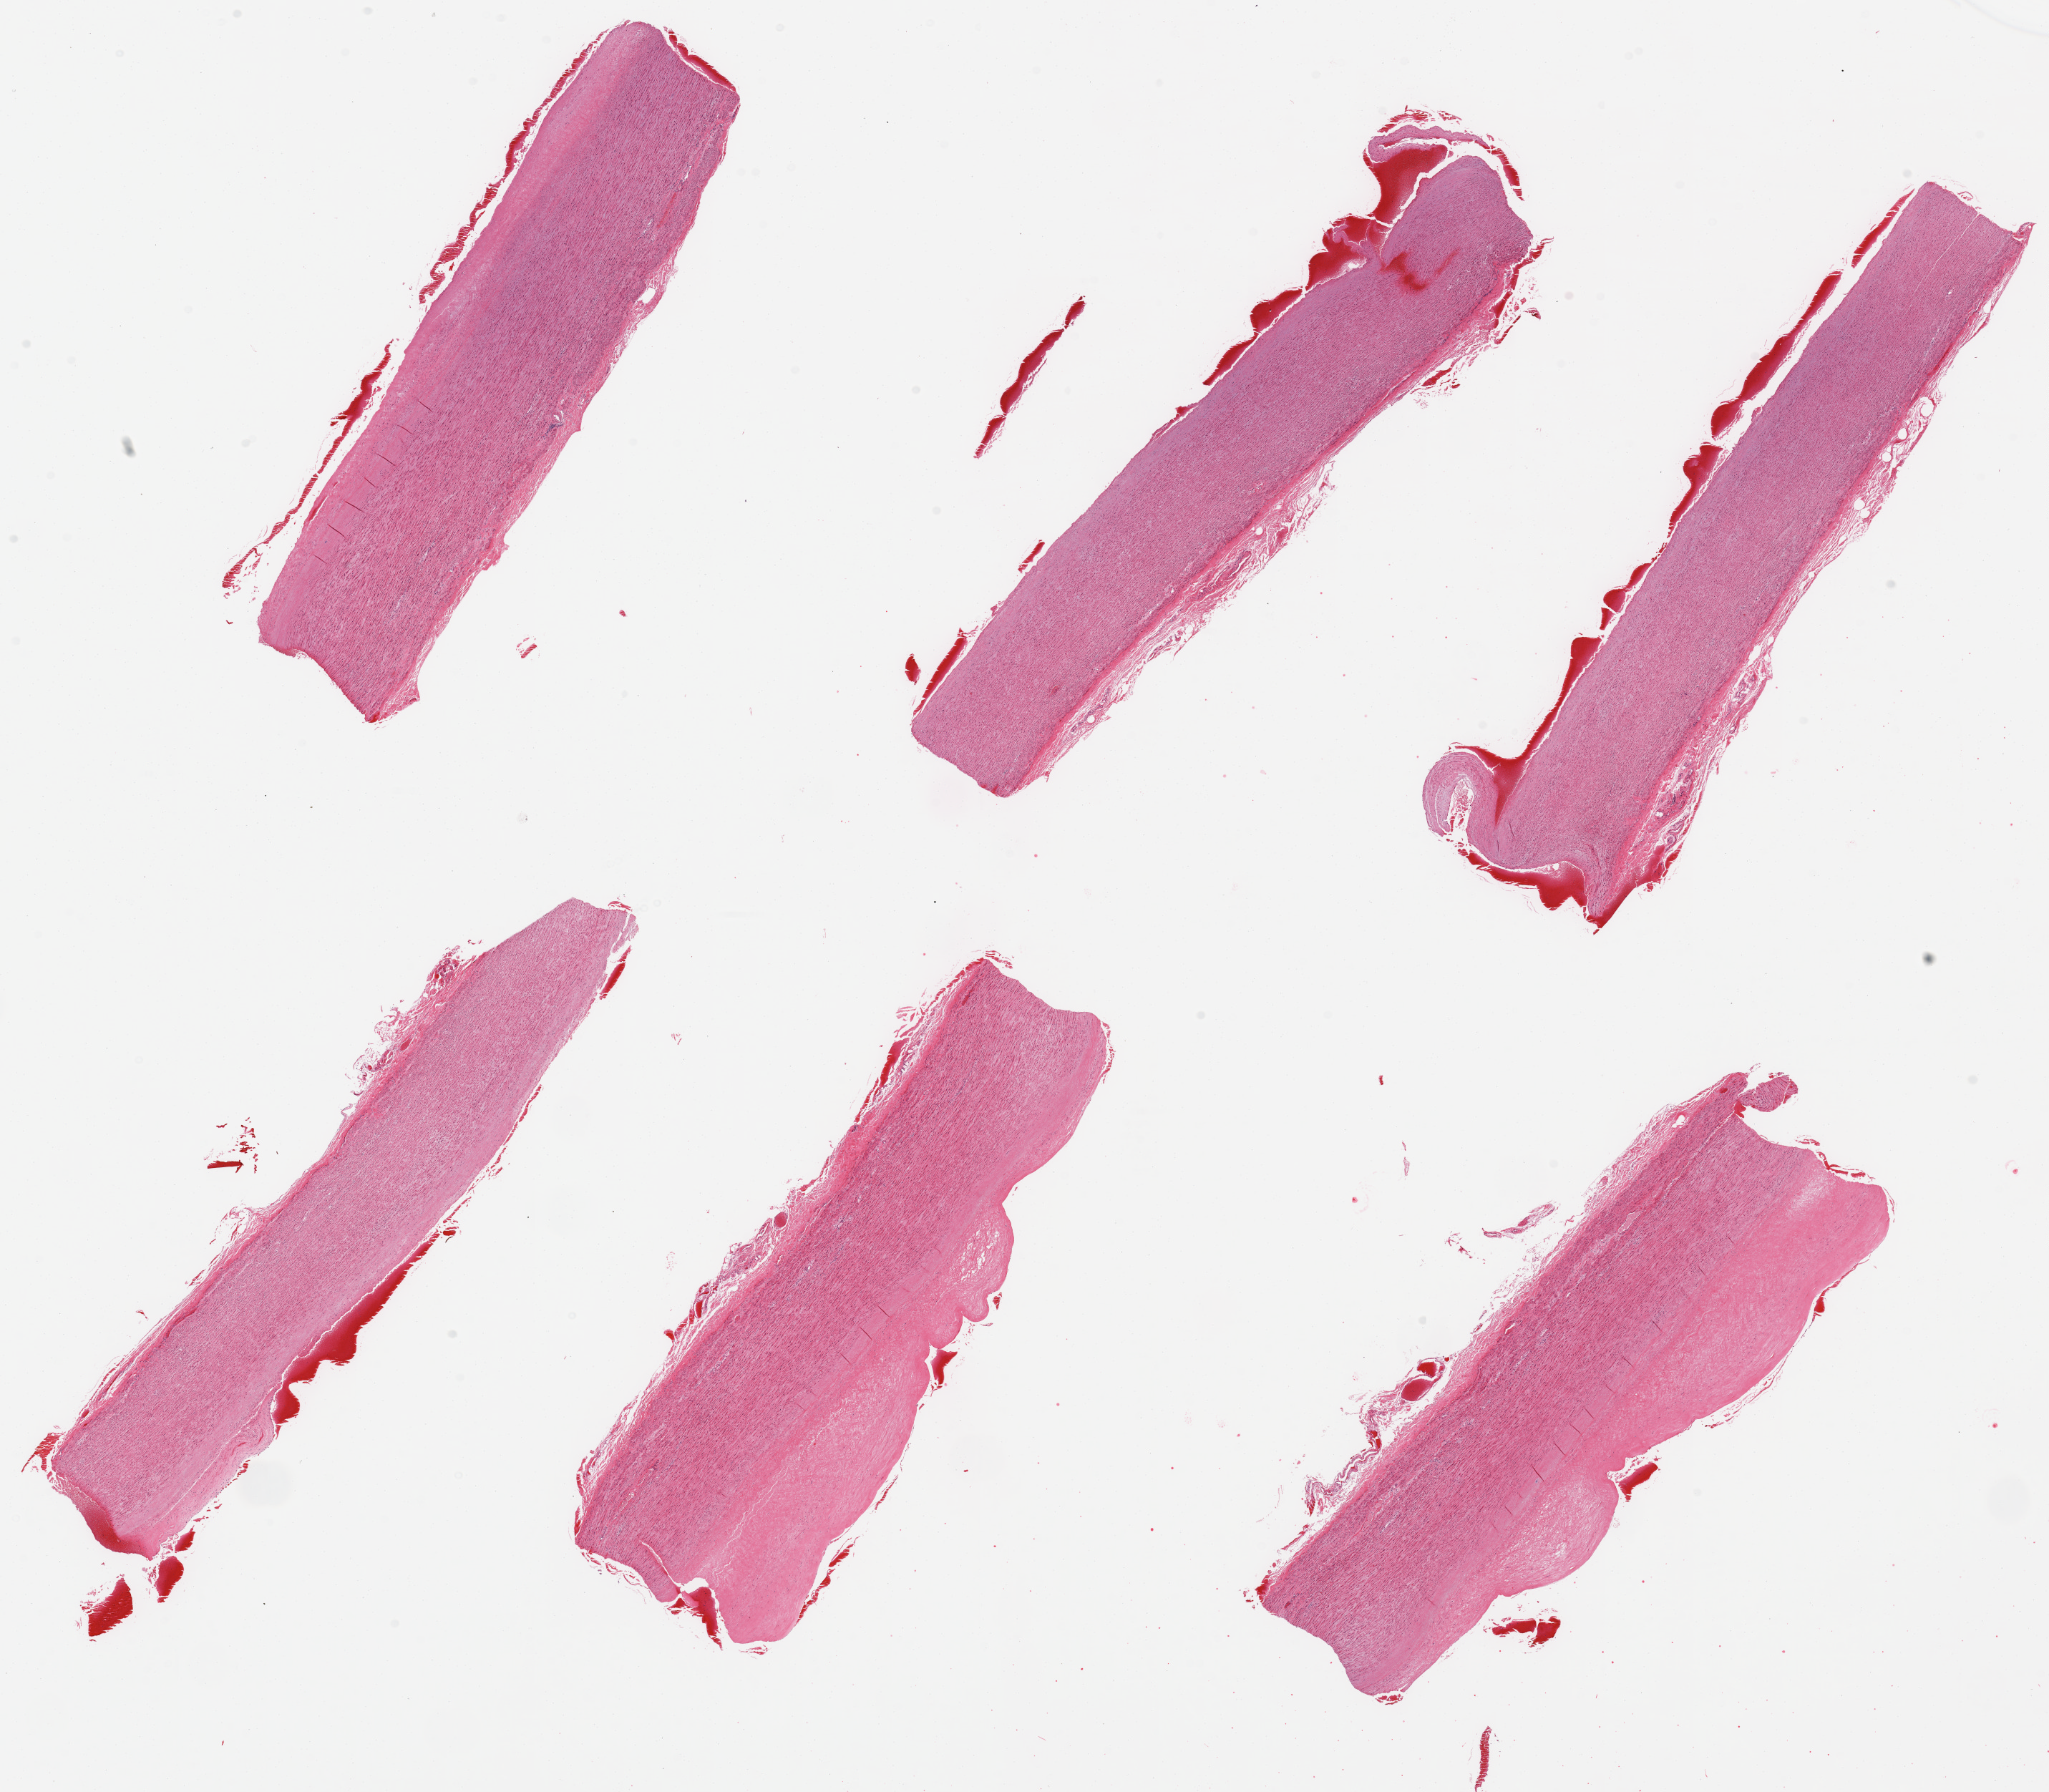
Digitized haematoxylin and eosin-stained section — low-resolution overview of the scanned area, about 22.6 x 19.8 mm (acquisition: 20x scan). PAXgene-fixed paraffin-embedded (PFPE) section. Target tissue: aorta. Donor tissue sample. Donor: male.
Review note (as recorded): 6 pieces; fibrosclerotic plaque more than 1mm thick.